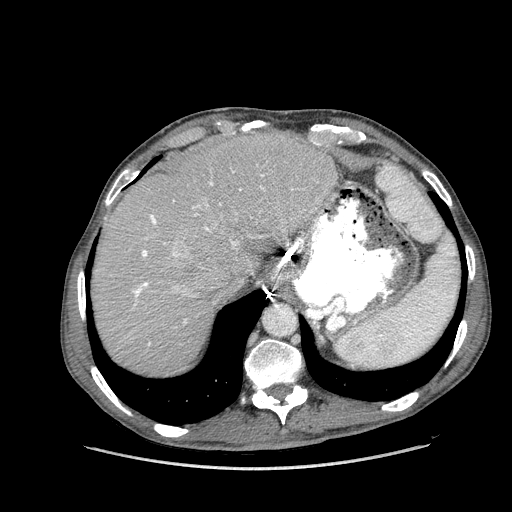
Contrast-enhanced abdominal CT (liver protocol), one axial slice. Position 117 of 162 along the scan axis. Soft-tissue window (W 400 / L 40 HU). 512 × 512 image matrix, field of view 400 × 400 mm. From the clinical record (not read from this slice): diagnosis: hepatocellular carcinoma (patient treated with transarterial chemoembolisation; whether this scan precedes or follows treatment is not stated here); TNM stage (as recorded): Stage-IIIA; Child-Pugh class: A.
Annotated regions visible in this slice (semi-automatically segmented with operator editing):
- abdominal aorta: bounding box (x1, y1, x2, y2) in pixels: (264, 304, 295, 335)
- liver parenchyma outside the tumour (the mass and vessels are separate outlines, so this box may not span the whole liver): (92, 132, 338, 374)
- mass: (169, 238, 208, 269)
- liver vessels: (133, 171, 264, 345)